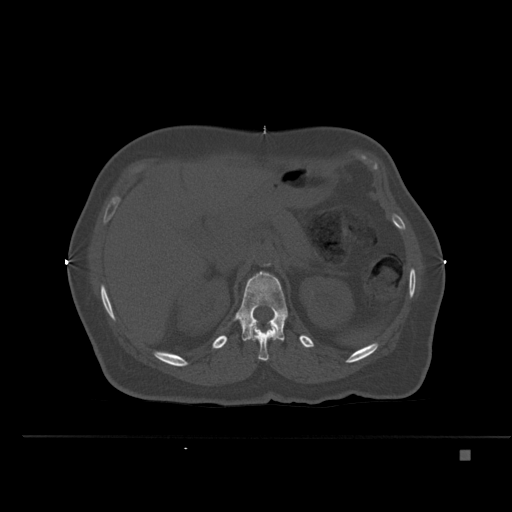
CT including the spine, one axial slice; position 242 of 477 along the scan axis; bone window (W 1800 / L 400 HU); 1.5 mm slice thickness; 512 × 512 image matrix, field of view 422 × 422 mm. Female patient, age 74 years. Case-level facts recorded for this patient, not image findings: primary cancer: colon.
Outlined on this slice (semi-automatic segmentation, software-assisted and operator-edited):
- L1 vertebra: bounding box [x1, y1, x2, y2] px = [235, 271, 288, 341]
- T12 vertebra: [249, 325, 278, 361]